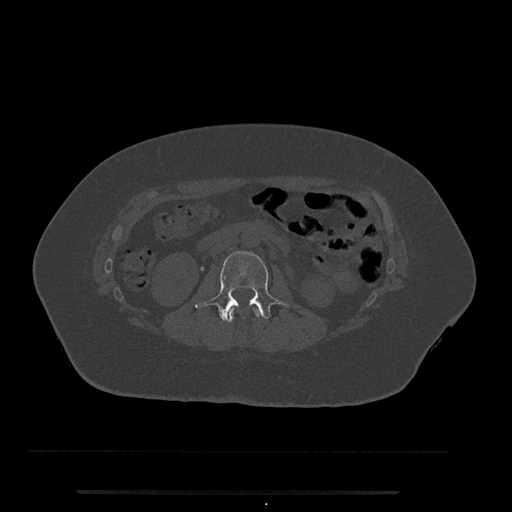
CT including the spine, one axial slice. Position 44 of 797 along the scan axis. Bone window (W 1800 / L 400 HU). 0.5 mm slice thickness. 512 × 512 image matrix, field of view 440 × 440 mm. Patient: female, 51 years. Case-level facts recorded for this patient, not image findings: primary cancer: neuro; vertebrae with lytic lesions (as recorded): T8.
Outlined on this slice (semi-automatically segmented with operator editing):
- L1 vertebra: bounding box (x1, y1, x2, y2) in pixels: (227, 307, 262, 323)
- L2 vertebra: (195, 251, 290, 321)